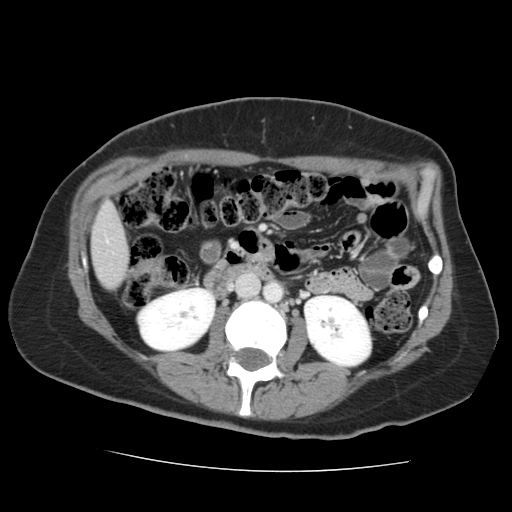
Contrast-enhanced abdominal CT, one axial slice. Slice 48 of 144 in the series (ordered by position). 120 kVp. Intravenous contrast given. Soft-tissue window (W 400 / L 40 HU). 2.5 mm slice thickness. 512 × 512 image matrix, field of view 333 × 333 mm. Female patient, age 46 years. Case-level facts recorded for this patient, not image findings: diagnosis: colorectal cancer liver metastases, imaged before liver resection; multiple liver metastases: no; largest metastasis: 2.8 cm; disease in both lobes: no.
Structures marked on this image (outlined manually by an expert reader):
- liver: bounding box <92,206,128,289> (left, top, right, bottom; pixels)
- planned liver remnant (the part of the liver to remain after resection): <93,206,121,289>